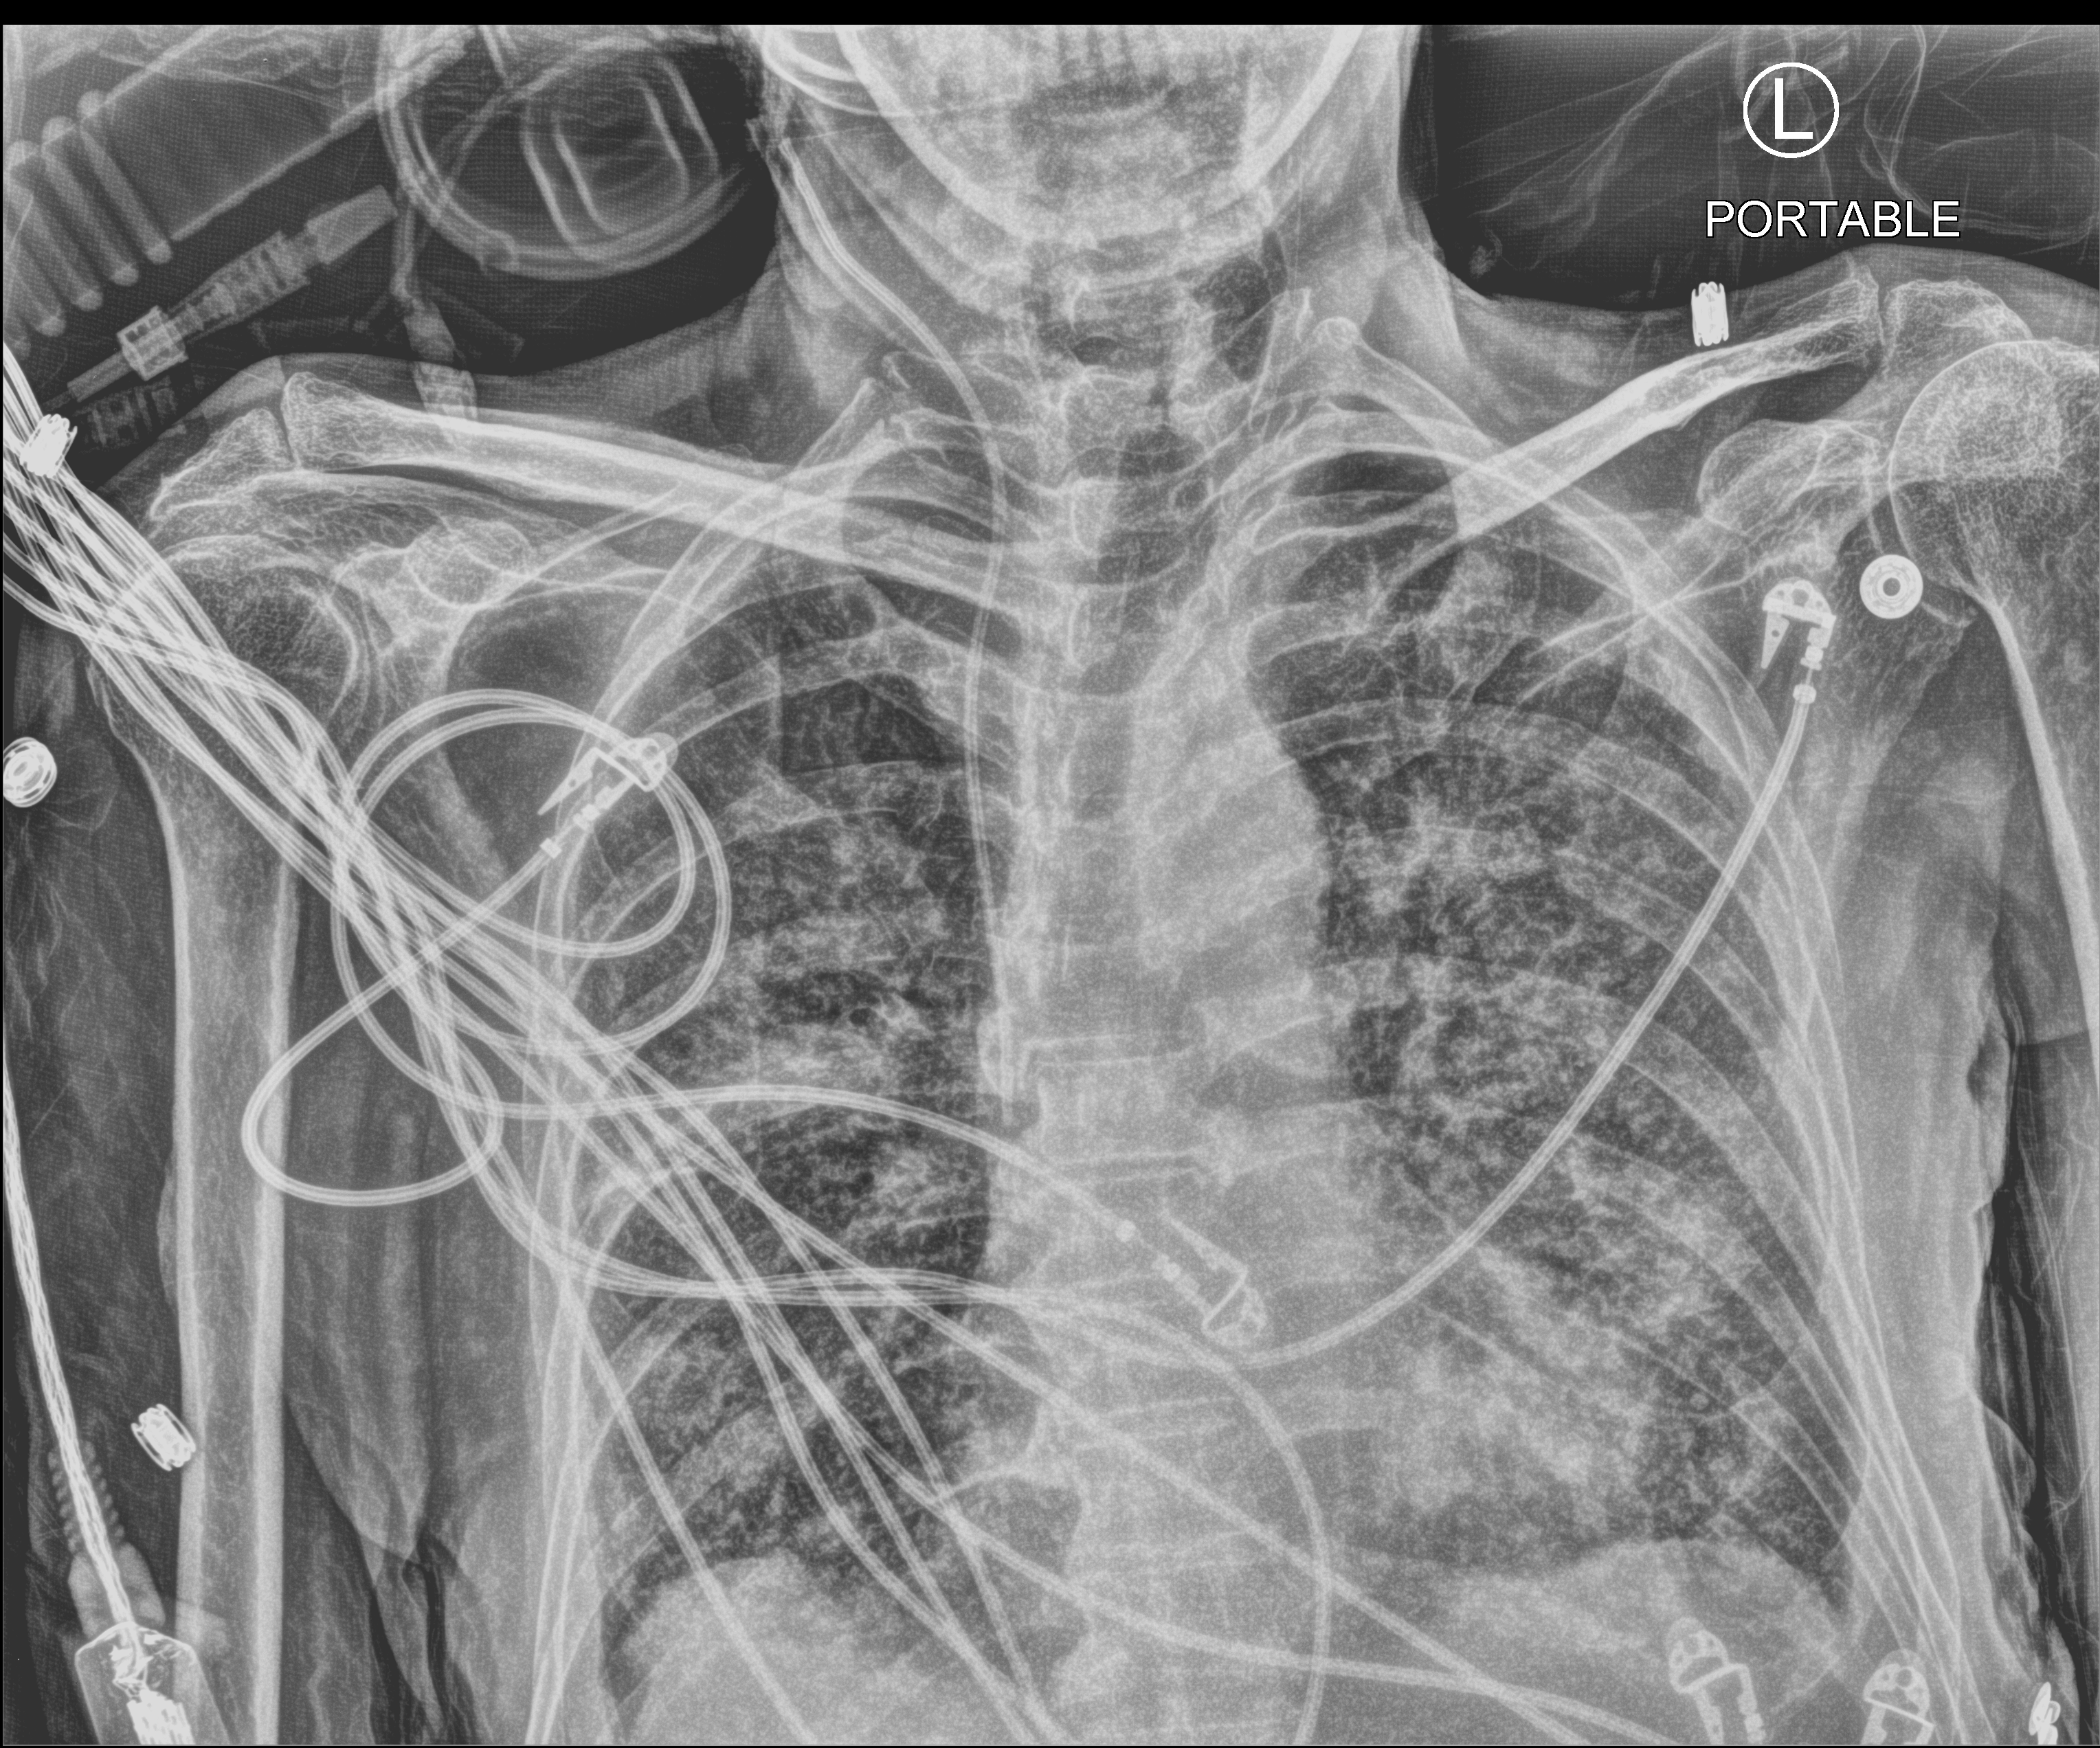
Bedside chest radiograph (computed radiography); anteroposterior (AP) projection. Patient hospitalised with COVID-19; male, aged 60–74 years.
Admission-level facts for this patient (not findings on this image; timing relative to this image not recorded): admitted to intensive care during this hospital stay: yes.